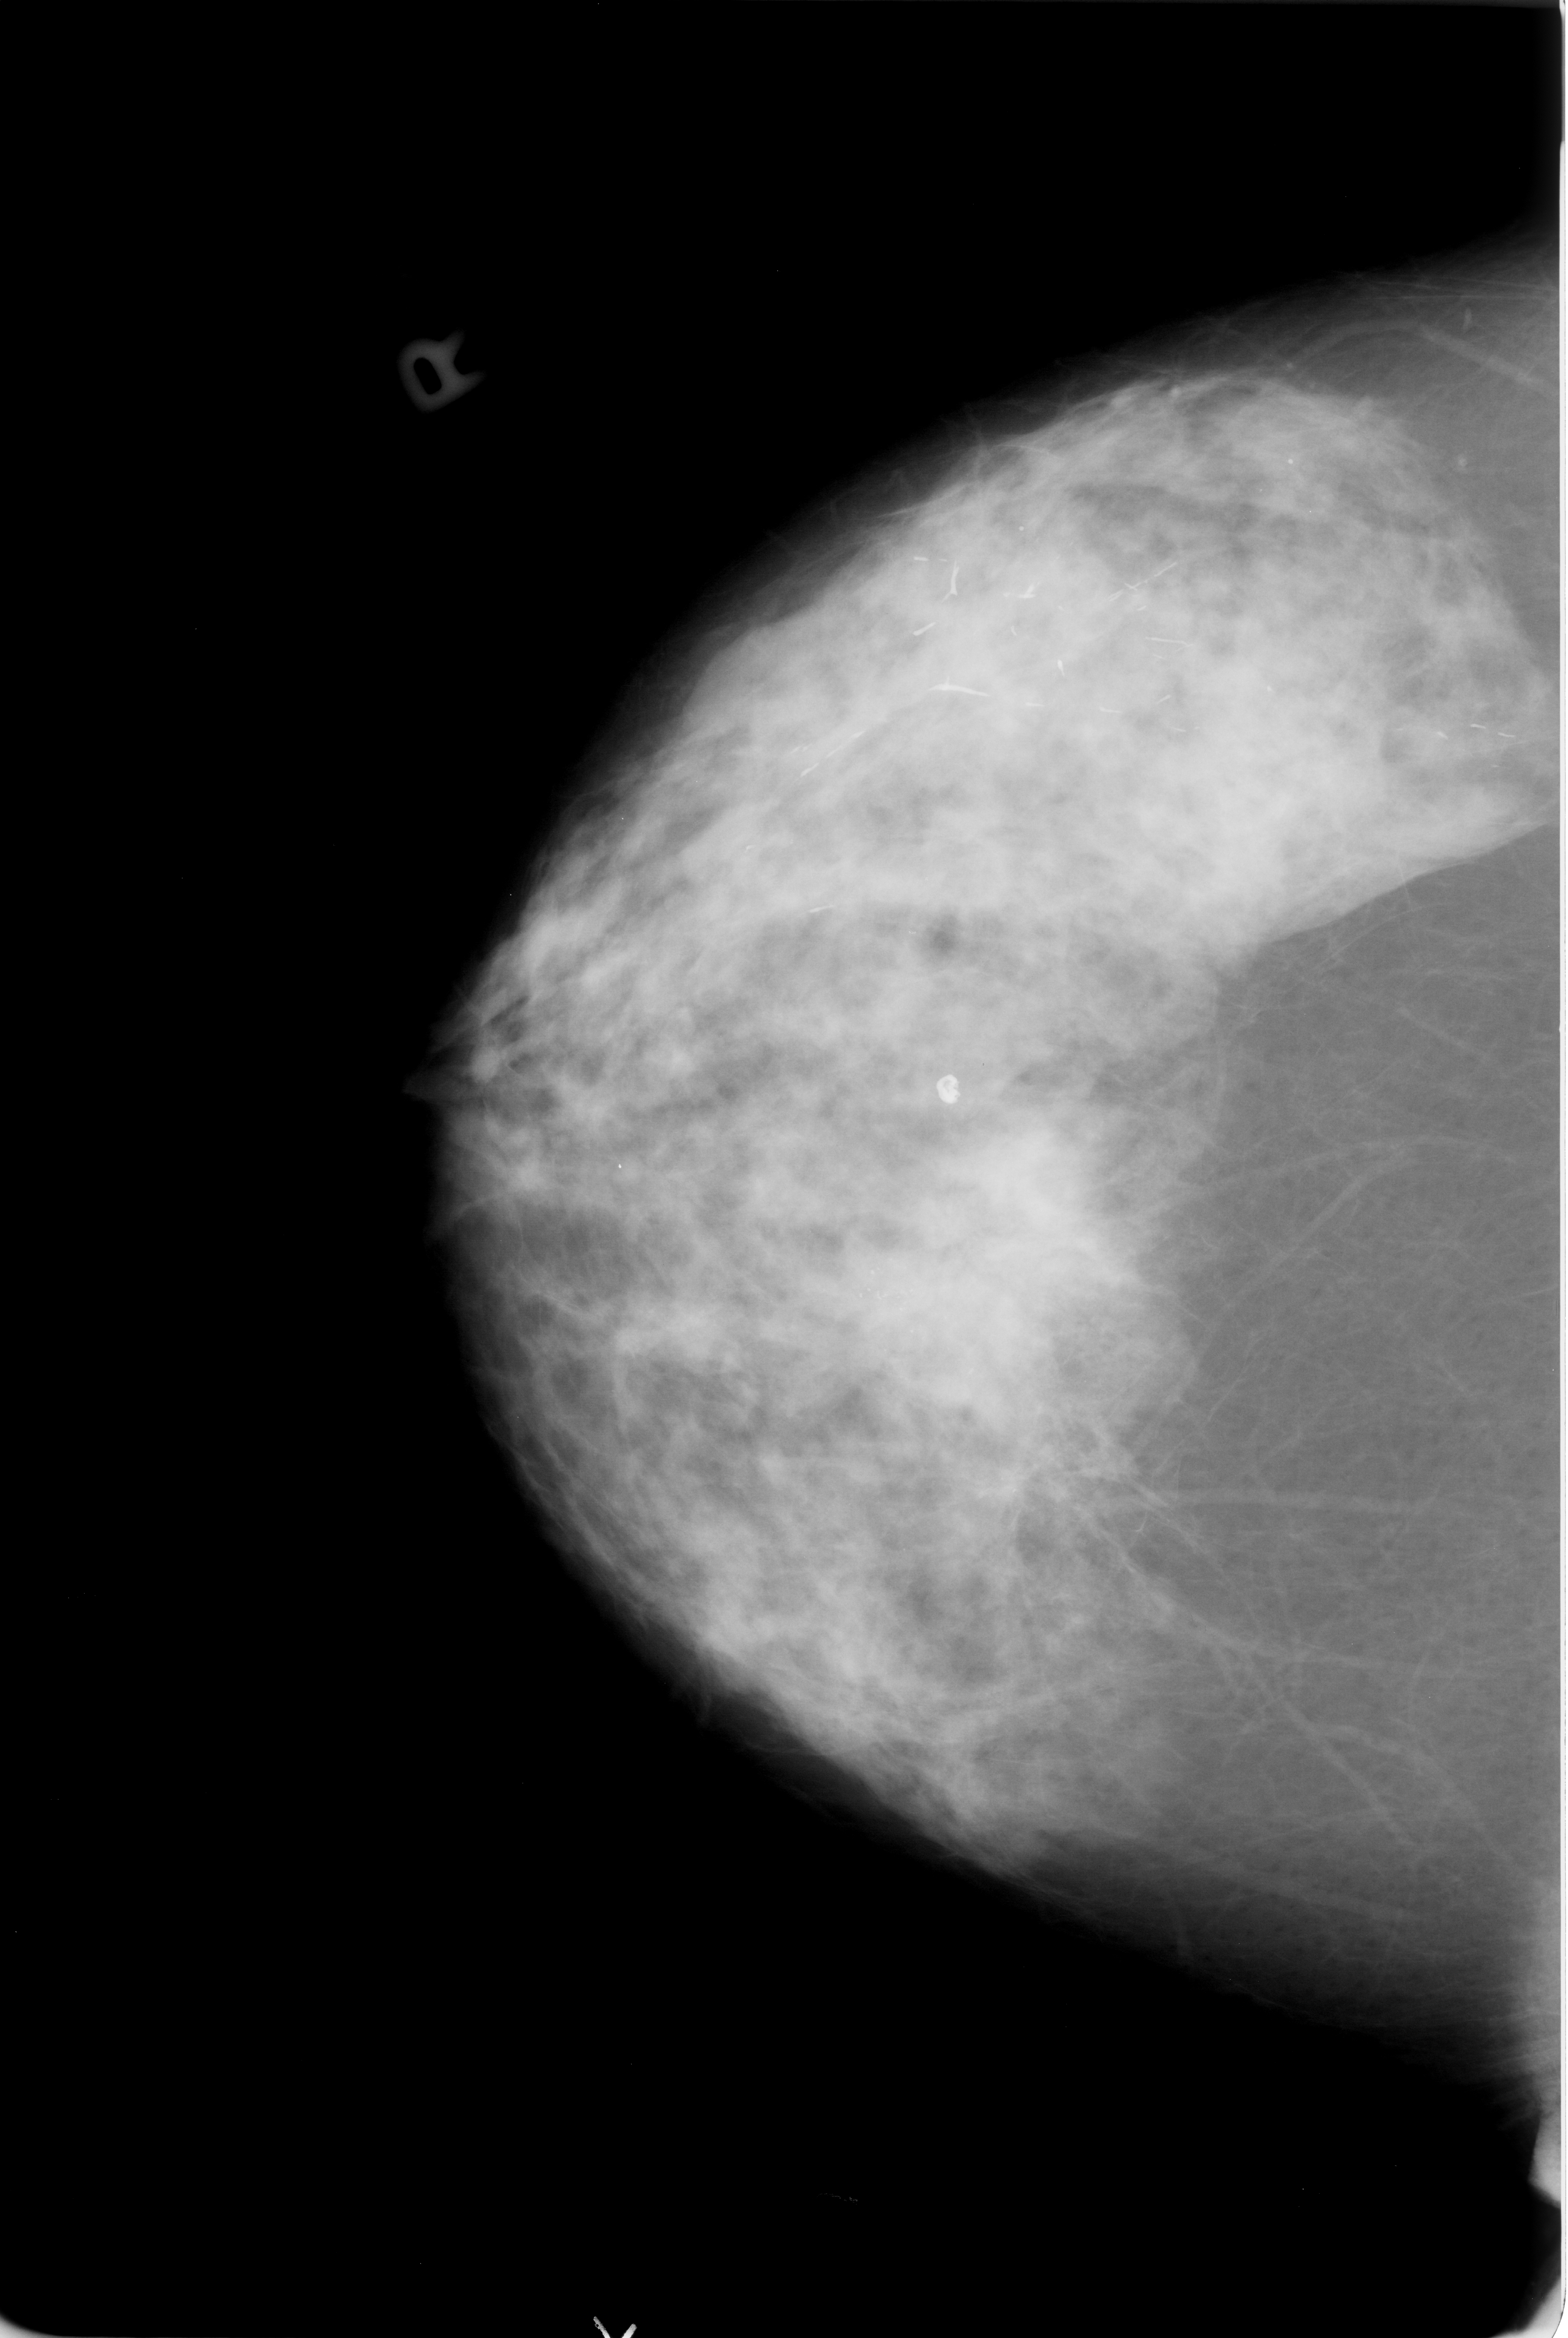
Digitized screen-film mammogram. Right breast. Craniocaudal (CC) view. Breast composition: heterogeneously dense (BI-RADS density category 3 of 4). 1568 × 2338 image matrix.
Marked abnormalities (boxes around the expert regions of interest):
- mass, shape architectural distortion, margins ill defined; BI-RADS assessment category 4; subtlety rating 3 on a 1 (subtle) to 5 (obvious) scale; pathology result (as recorded, not read from the image): malignant: bounding box [x1, y1, x2, y2] px = [839, 1148, 1110, 1395]